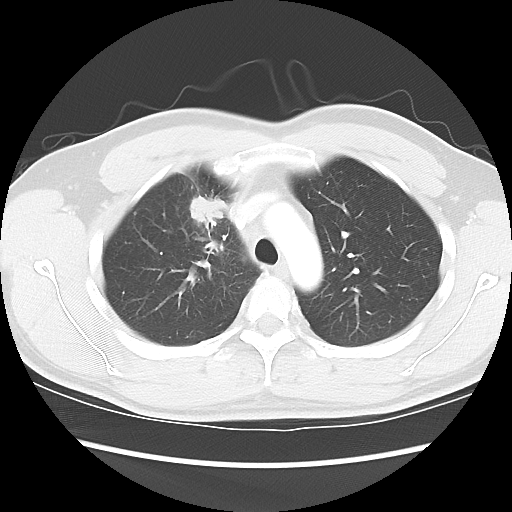
Chest CT, one axial slice. Position 66 of 80 along the scan axis. Reconstruction kernel LUNG. 120 kVp. Lung window (W 1500 / L -600 HU). 512 × 512 image matrix, field of view 360 × 360 mm. Male patient, age 35 years. Case-level facts recorded for this patient, not image findings: clinical TNM (as recorded): T1c N1 M1b.
Outlined on this slice (rectangle marked by the reading radiologist):
- lung tumour (recorded histology: adenocarcinoma): bounding box <185,192,230,227> (left, top, right, bottom; pixels)